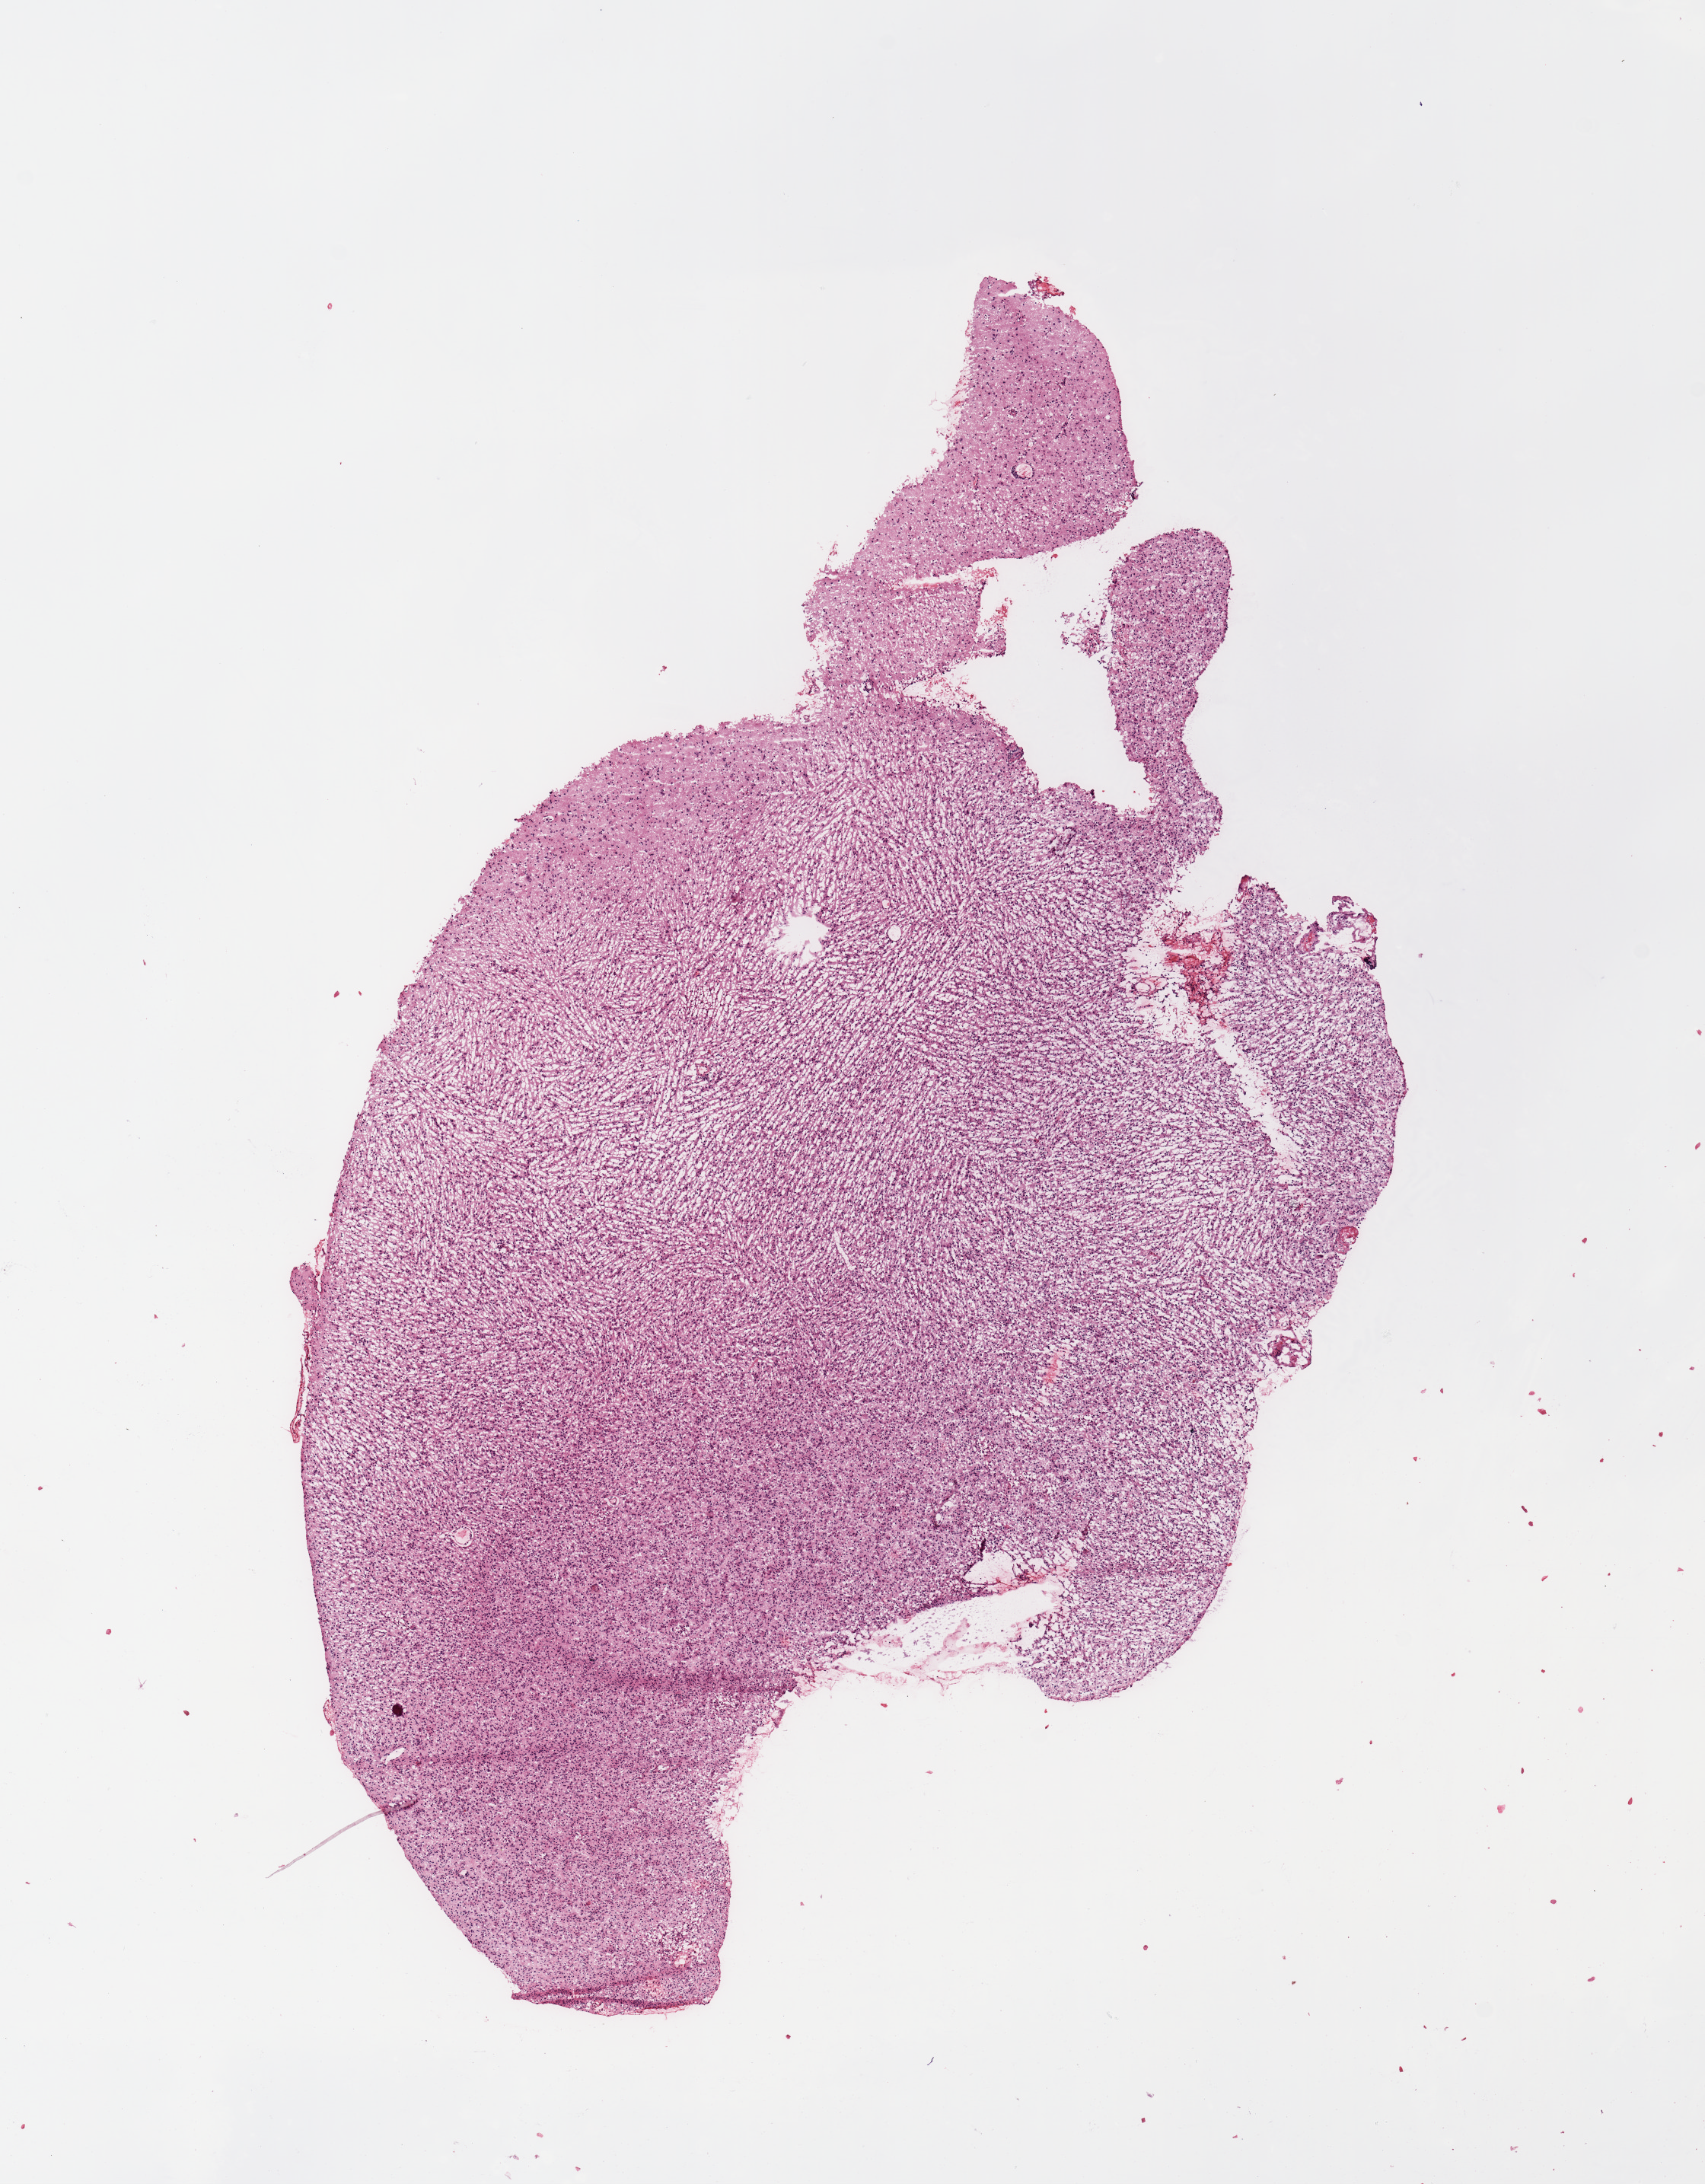
Whole-slide histology image, Hematoxylin and eosin (H&E) stained — a low-resolution overview of the entire scanned area, about 8.9 x 11.3 mm (from a 20x scan). Tumour tissue sample, brain. Patient: female, age 49 years.
Primary tumour site (as recorded): parietal lobe. Patient diagnosis (cohort enrolment): glioblastoma multiforme (brain).